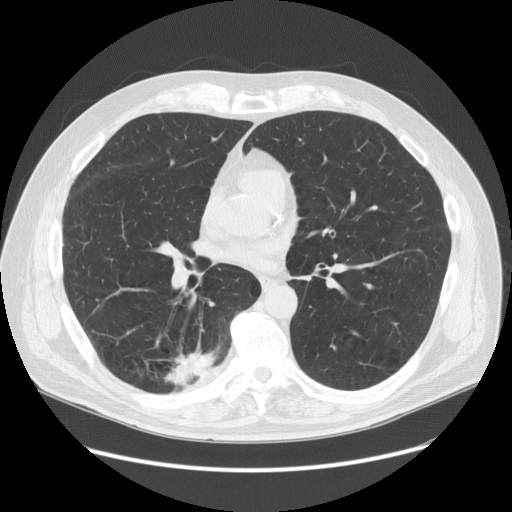
Low-dose screening chest CT, axial slice; baseline annual screen; lung window (W 1500 / L -600 HU); standard (soft-tissue) reconstruction kernel (STANDARD). Male participant, aged 68 years at enrolment. Former smoker at enrolment.
Expert-annotated lung lesion, bounding box (x1, y1, x2, y2) in pixels: (126, 339, 225, 412). The exam's reader record, not a measurement of the box and not confirmed to be the same lesion: non-calcified nodule or mass ≥4 mm, right lower lobe, 37 × 20 mm, spiculated (stellate) margins, soft tissue attenuation. Official screen result: positive, change unspecified: nodule(s) >= 4 mm or enlarging nodule(s), mass(es), or other non-specific abnormalities suspicious for lung cancer. Lung cancer was diagnosed 24 days after this screen: adenosquamous carcinoma, right lower lobe, poorly differentiated (G3), stage IIIA (AJCC 6th edition), 30 mm at pathology.